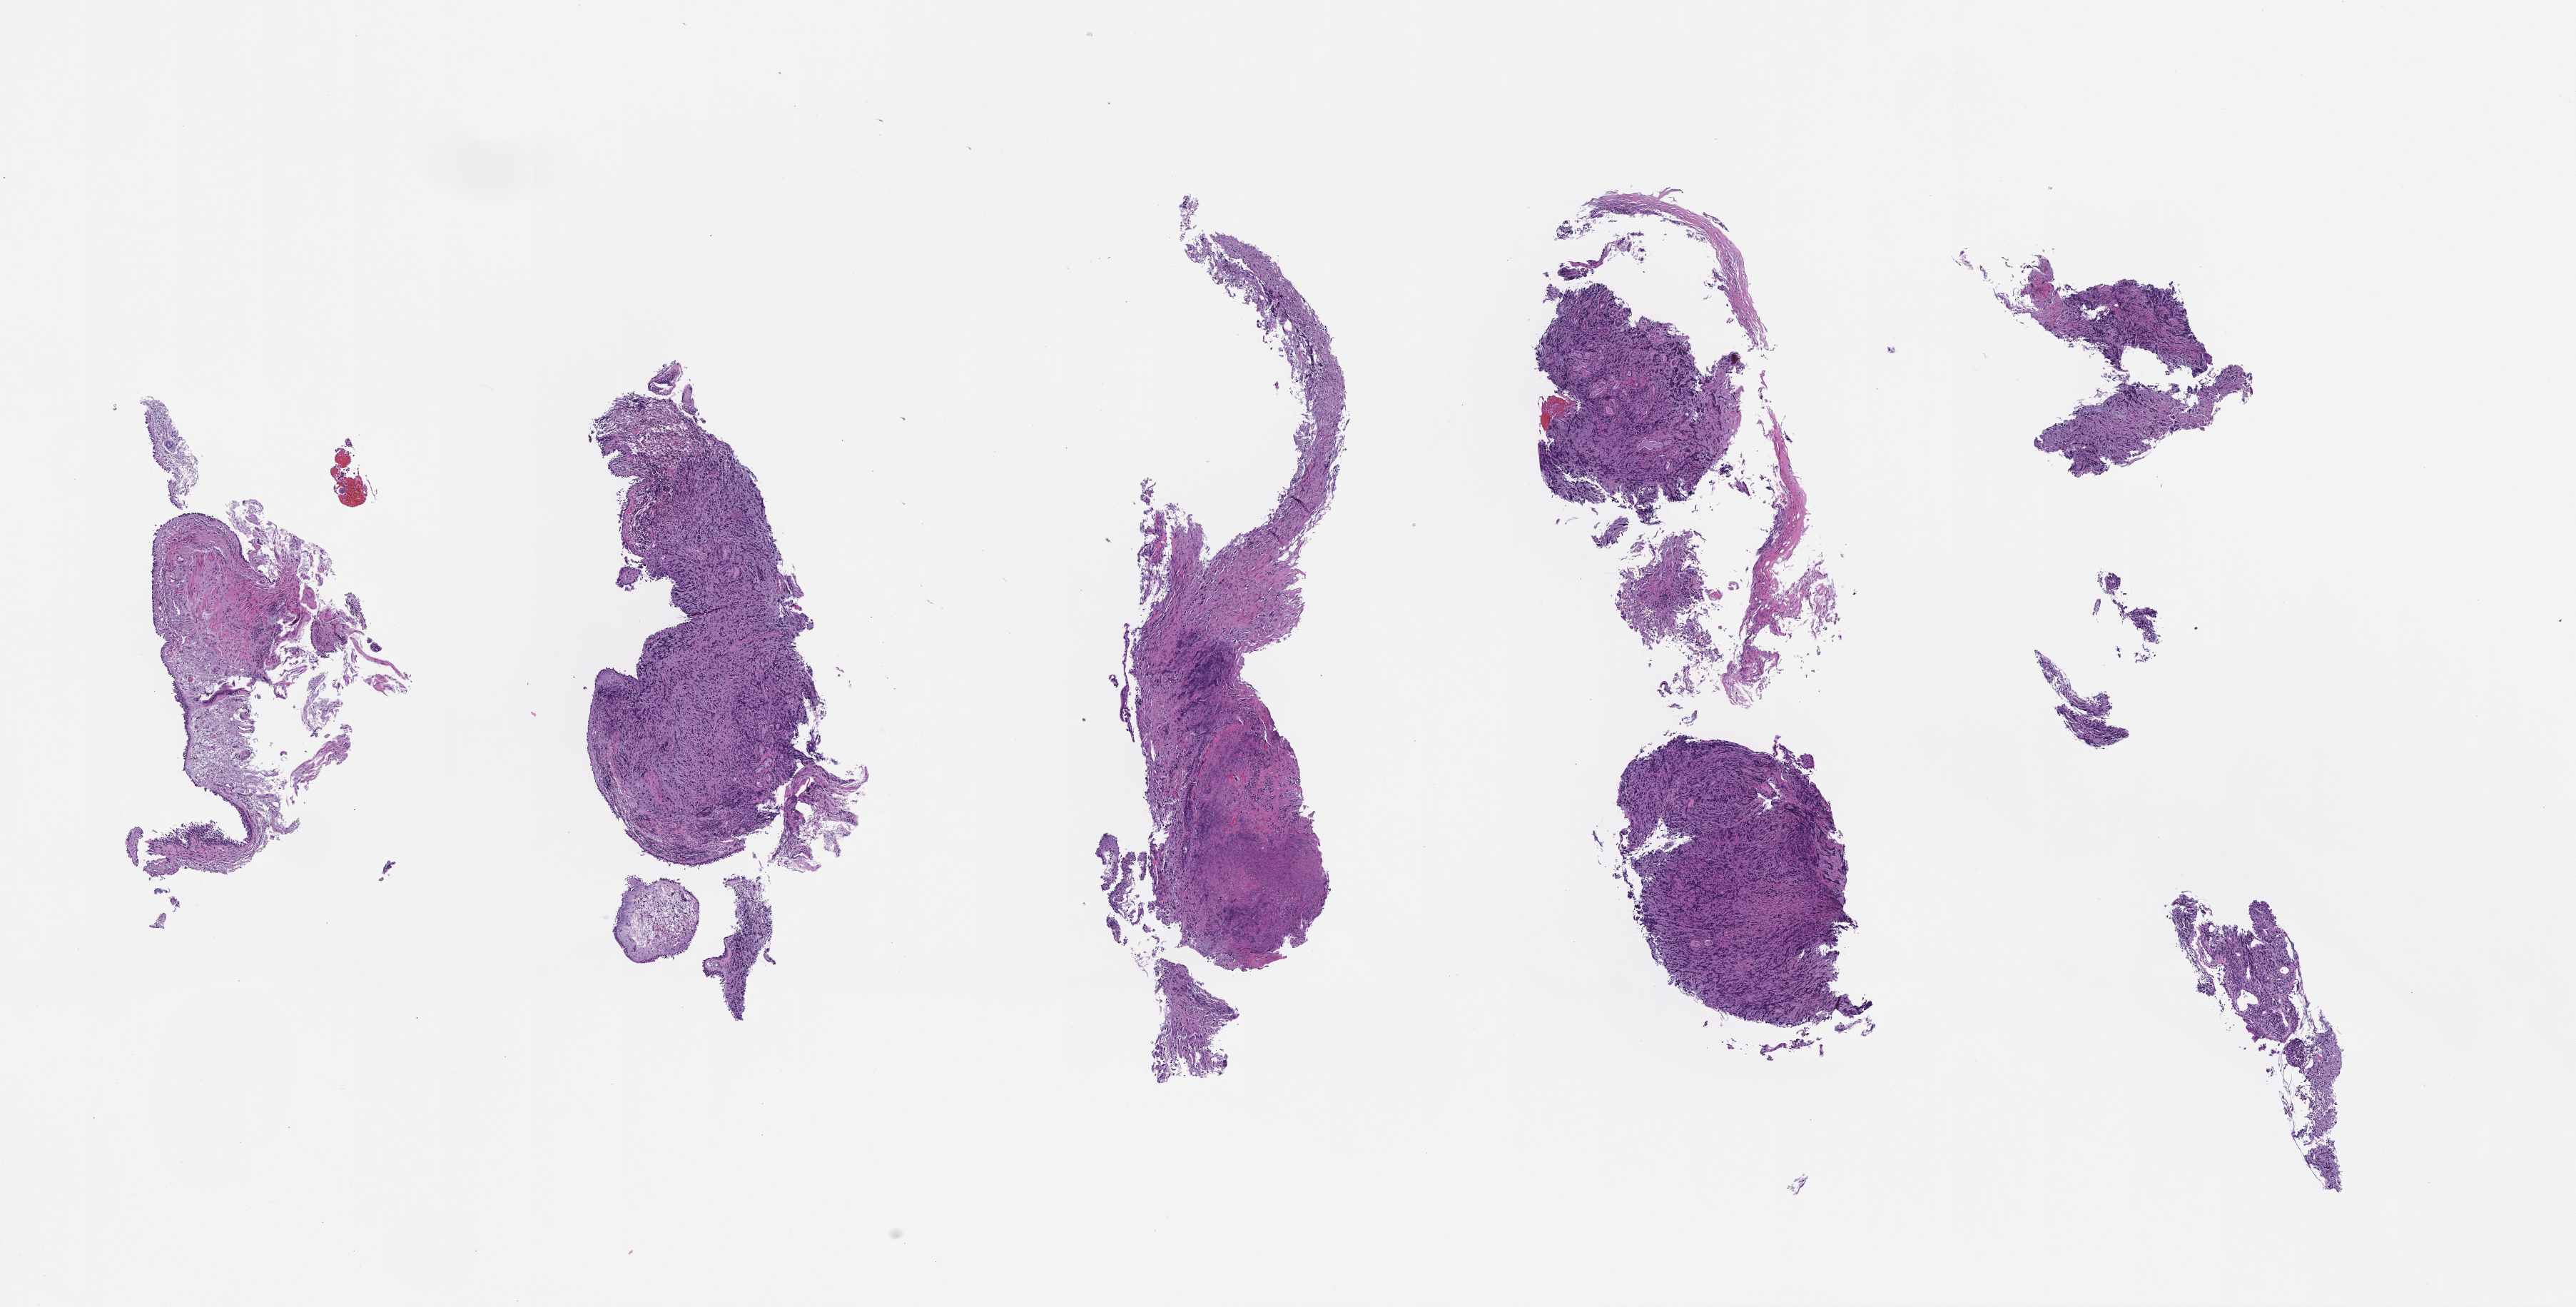
Whole-slide image, haematoxylin and eosin stain, whole scanned area (about 14.6 x 7.4 mm) shown as a low-resolution overview; FFPE section; tissue site: lung; specimen time point: archival tissue. Female patient.
* this section: primary tumor
* diagnosis: Non-Small Cell Lung Carcinoma